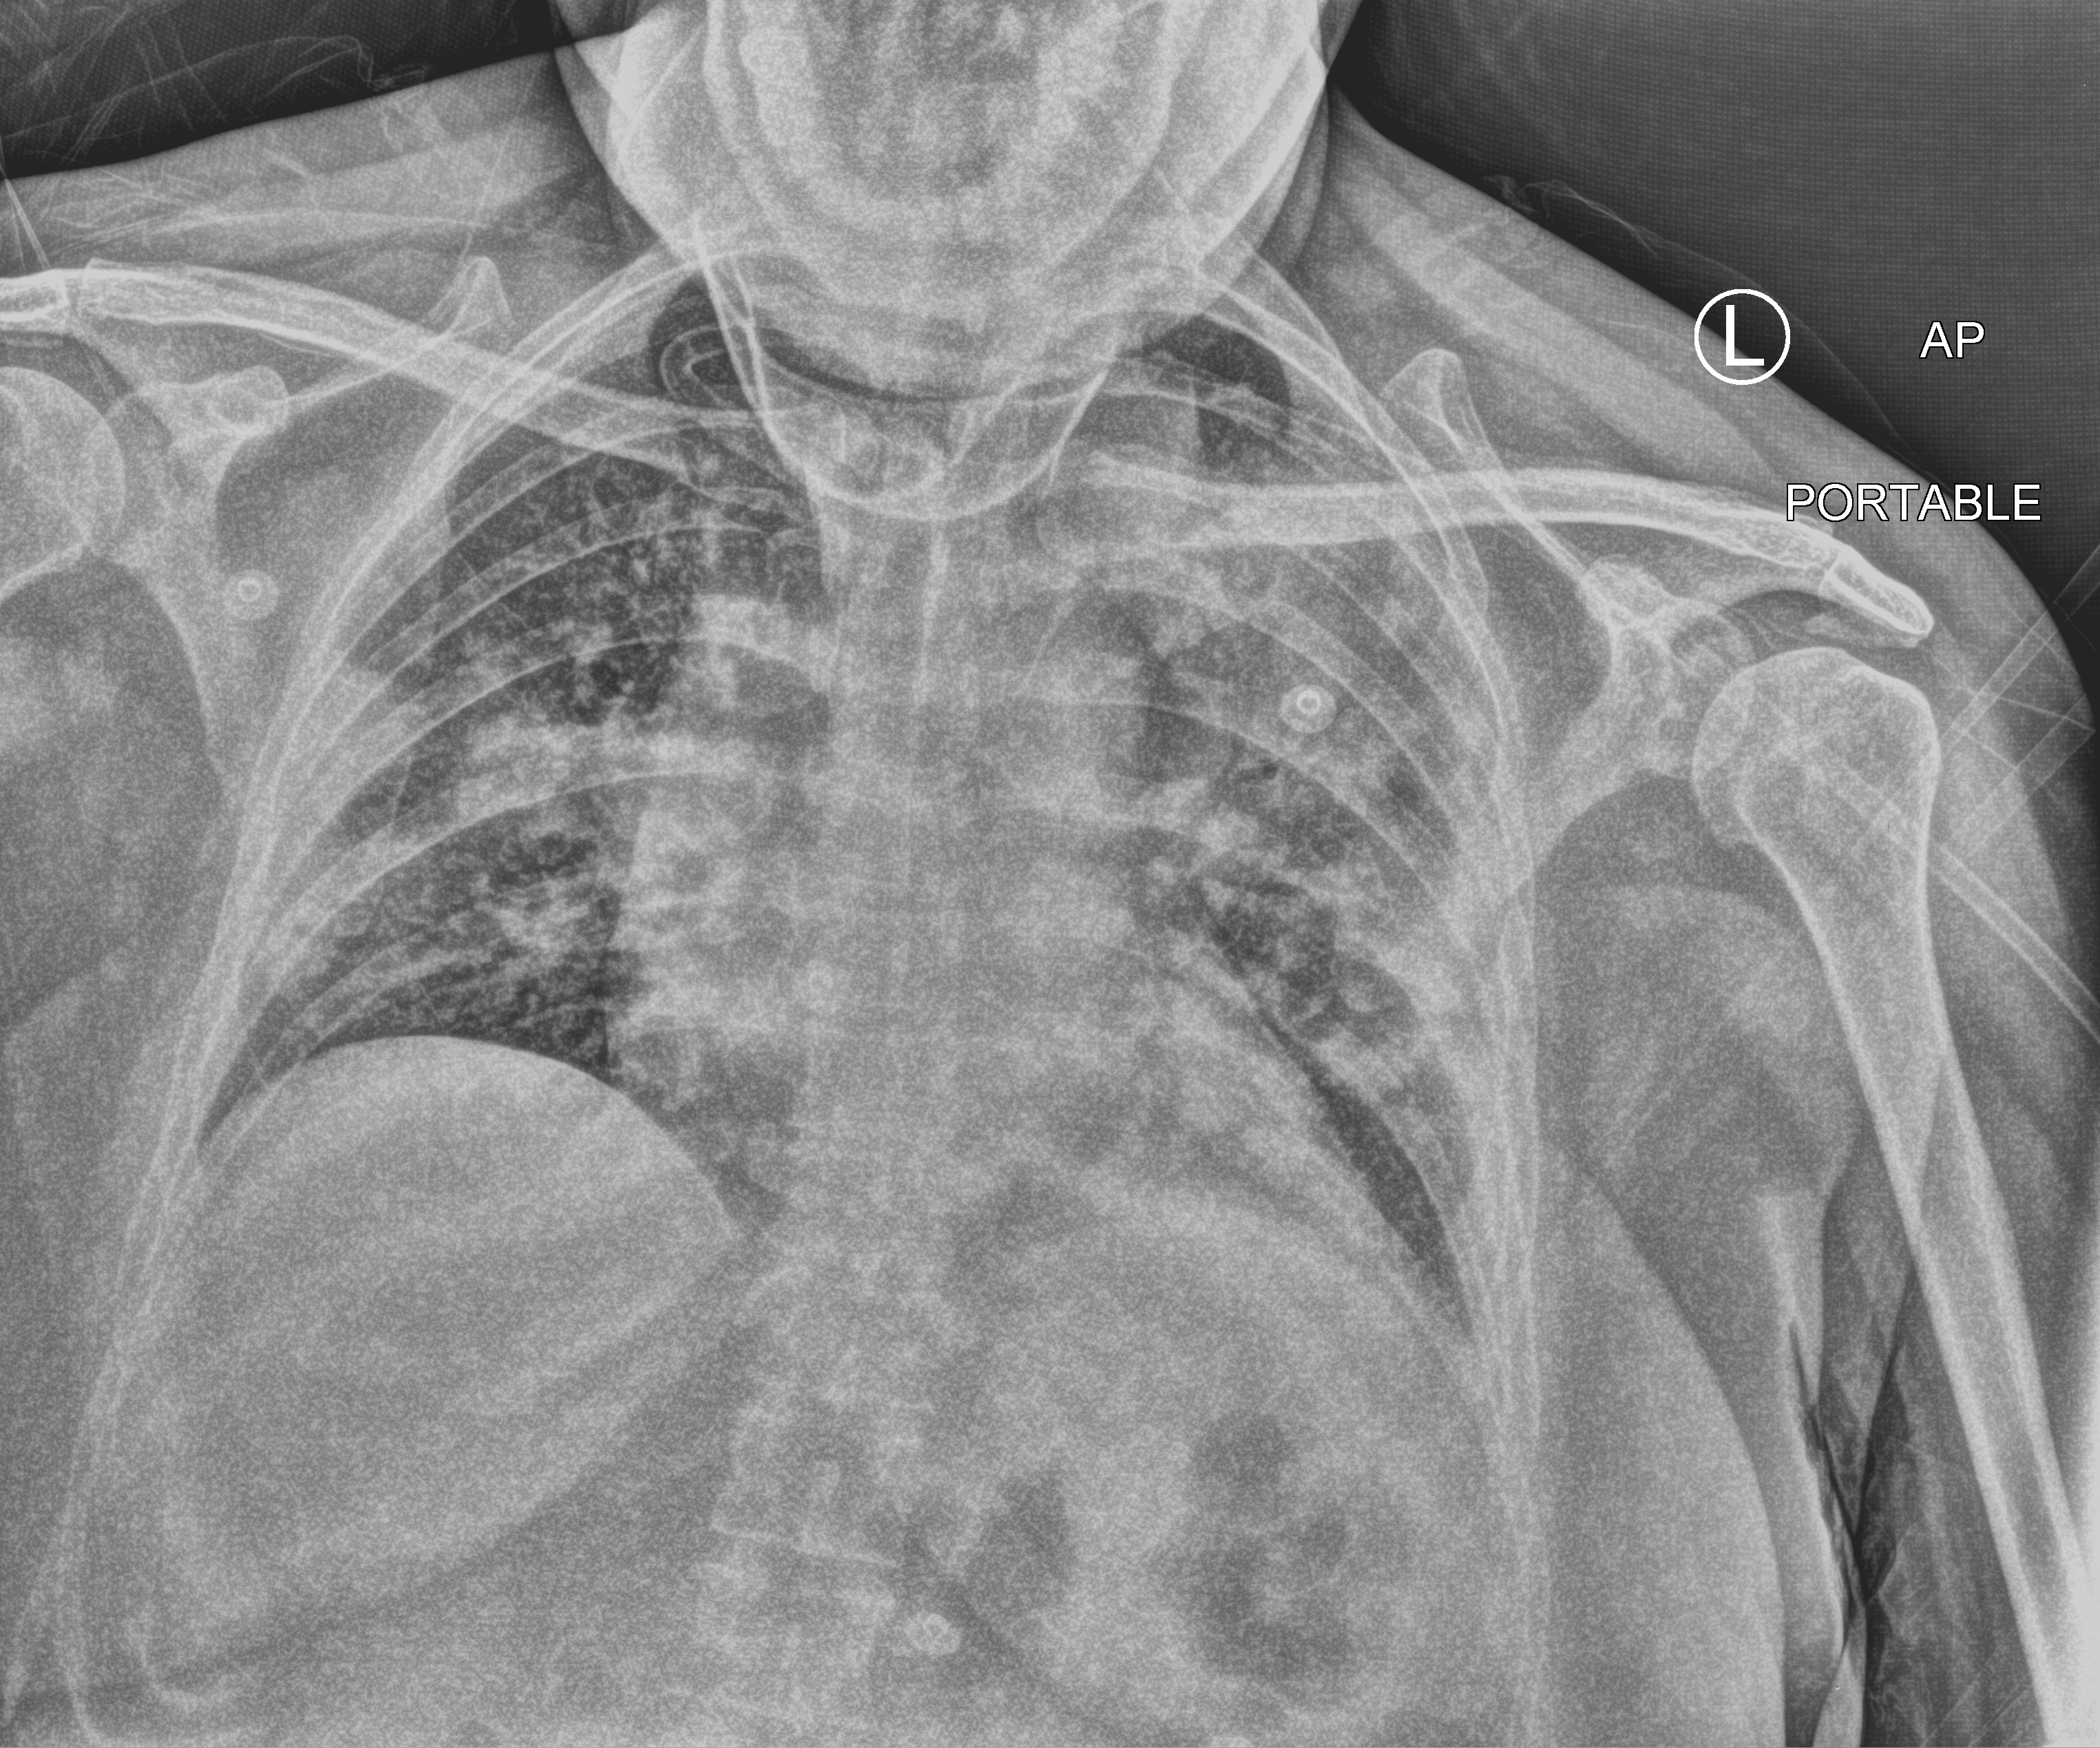
Chest X-ray (portable), anteroposterior (AP) projection. Female patient hospitalised with COVID-19, age 18–59 years.
From the hospital-stay record, not from the radiograph (when in the stay this image was taken is not recorded): mechanically ventilated during this hospital stay: yes.